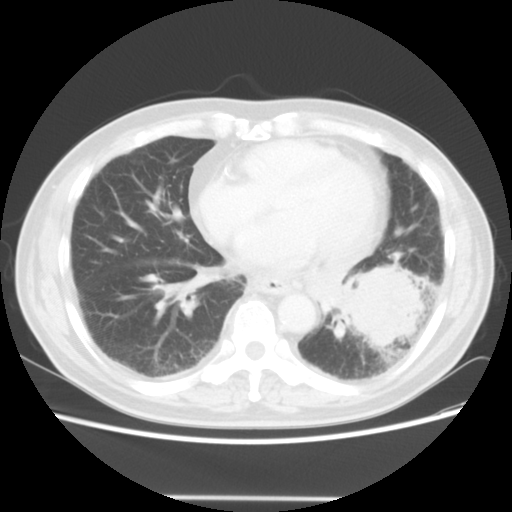
Chest CT, one axial slice. Position 18 of 56 along the scan axis. Reconstruction kernel STANDARD. 140 kVp. Lung window (W 1500 / L -600 HU). 5 mm slice thickness. 512 × 512 image matrix, field of view 360 × 360 mm. Patient: male, 66 years. Case-level facts recorded for this patient, not image findings: clinical TNM (as recorded): T4 N3 M0.
Outlined on this slice (bounding box drawn by a radiologist):
- lung tumour (recorded histology: small cell carcinoma): bounding box [x1, y1, x2, y2] px = [336, 266, 430, 348]